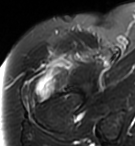
MRI of an extremity soft-tissue mass, one axial slice; slice 83 of 95 in the series (ordered by position); T2-weighted fat-saturated; MR volume resampled by the dataset authors to the PET/CT grid (not the native acquisition matrix); 135 × 146 image matrix, field of view 132 × 143 mm. Female patient. Case-level facts recorded for this patient, not image findings: histological type: pleiomorphic undifferentiated sarcoma; grade: high; site of the primary tumour: right quadricep.
Annotated regions visible in this slice (expert contour drawn on MRI and transferred to this co-registered scan by the dataset authors):
- gross tumour volume including surrounding oedema: box from (x=34, y=66) to (x=61, y=103) px